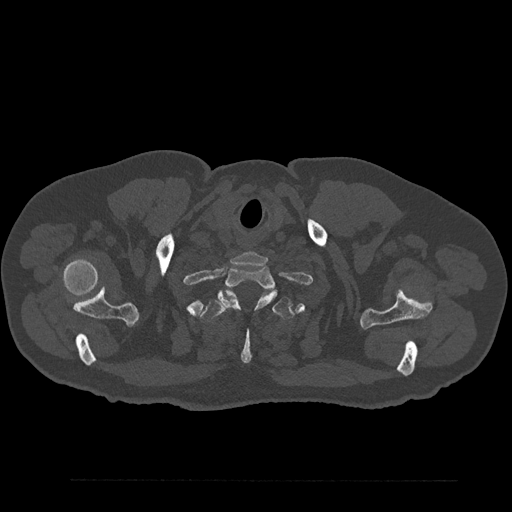
CT including the spine, one axial slice. Slice 742 of 797 in the series (ordered by position). 120 kVp. Bone window (W 1800 / L 400 HU). 0.5 mm slice thickness. 512 × 512 image matrix. Male patient, age 61 years. Case-level facts recorded for this patient, not image findings: primary cancer: prostate.
Annotated regions visible in this slice (semi-automatically segmented with operator editing):
- T1 vertebra: bounding box [x1, y1, x2, y2] px = [218, 266, 276, 309]
- T2 vertebra: [200, 291, 295, 364]